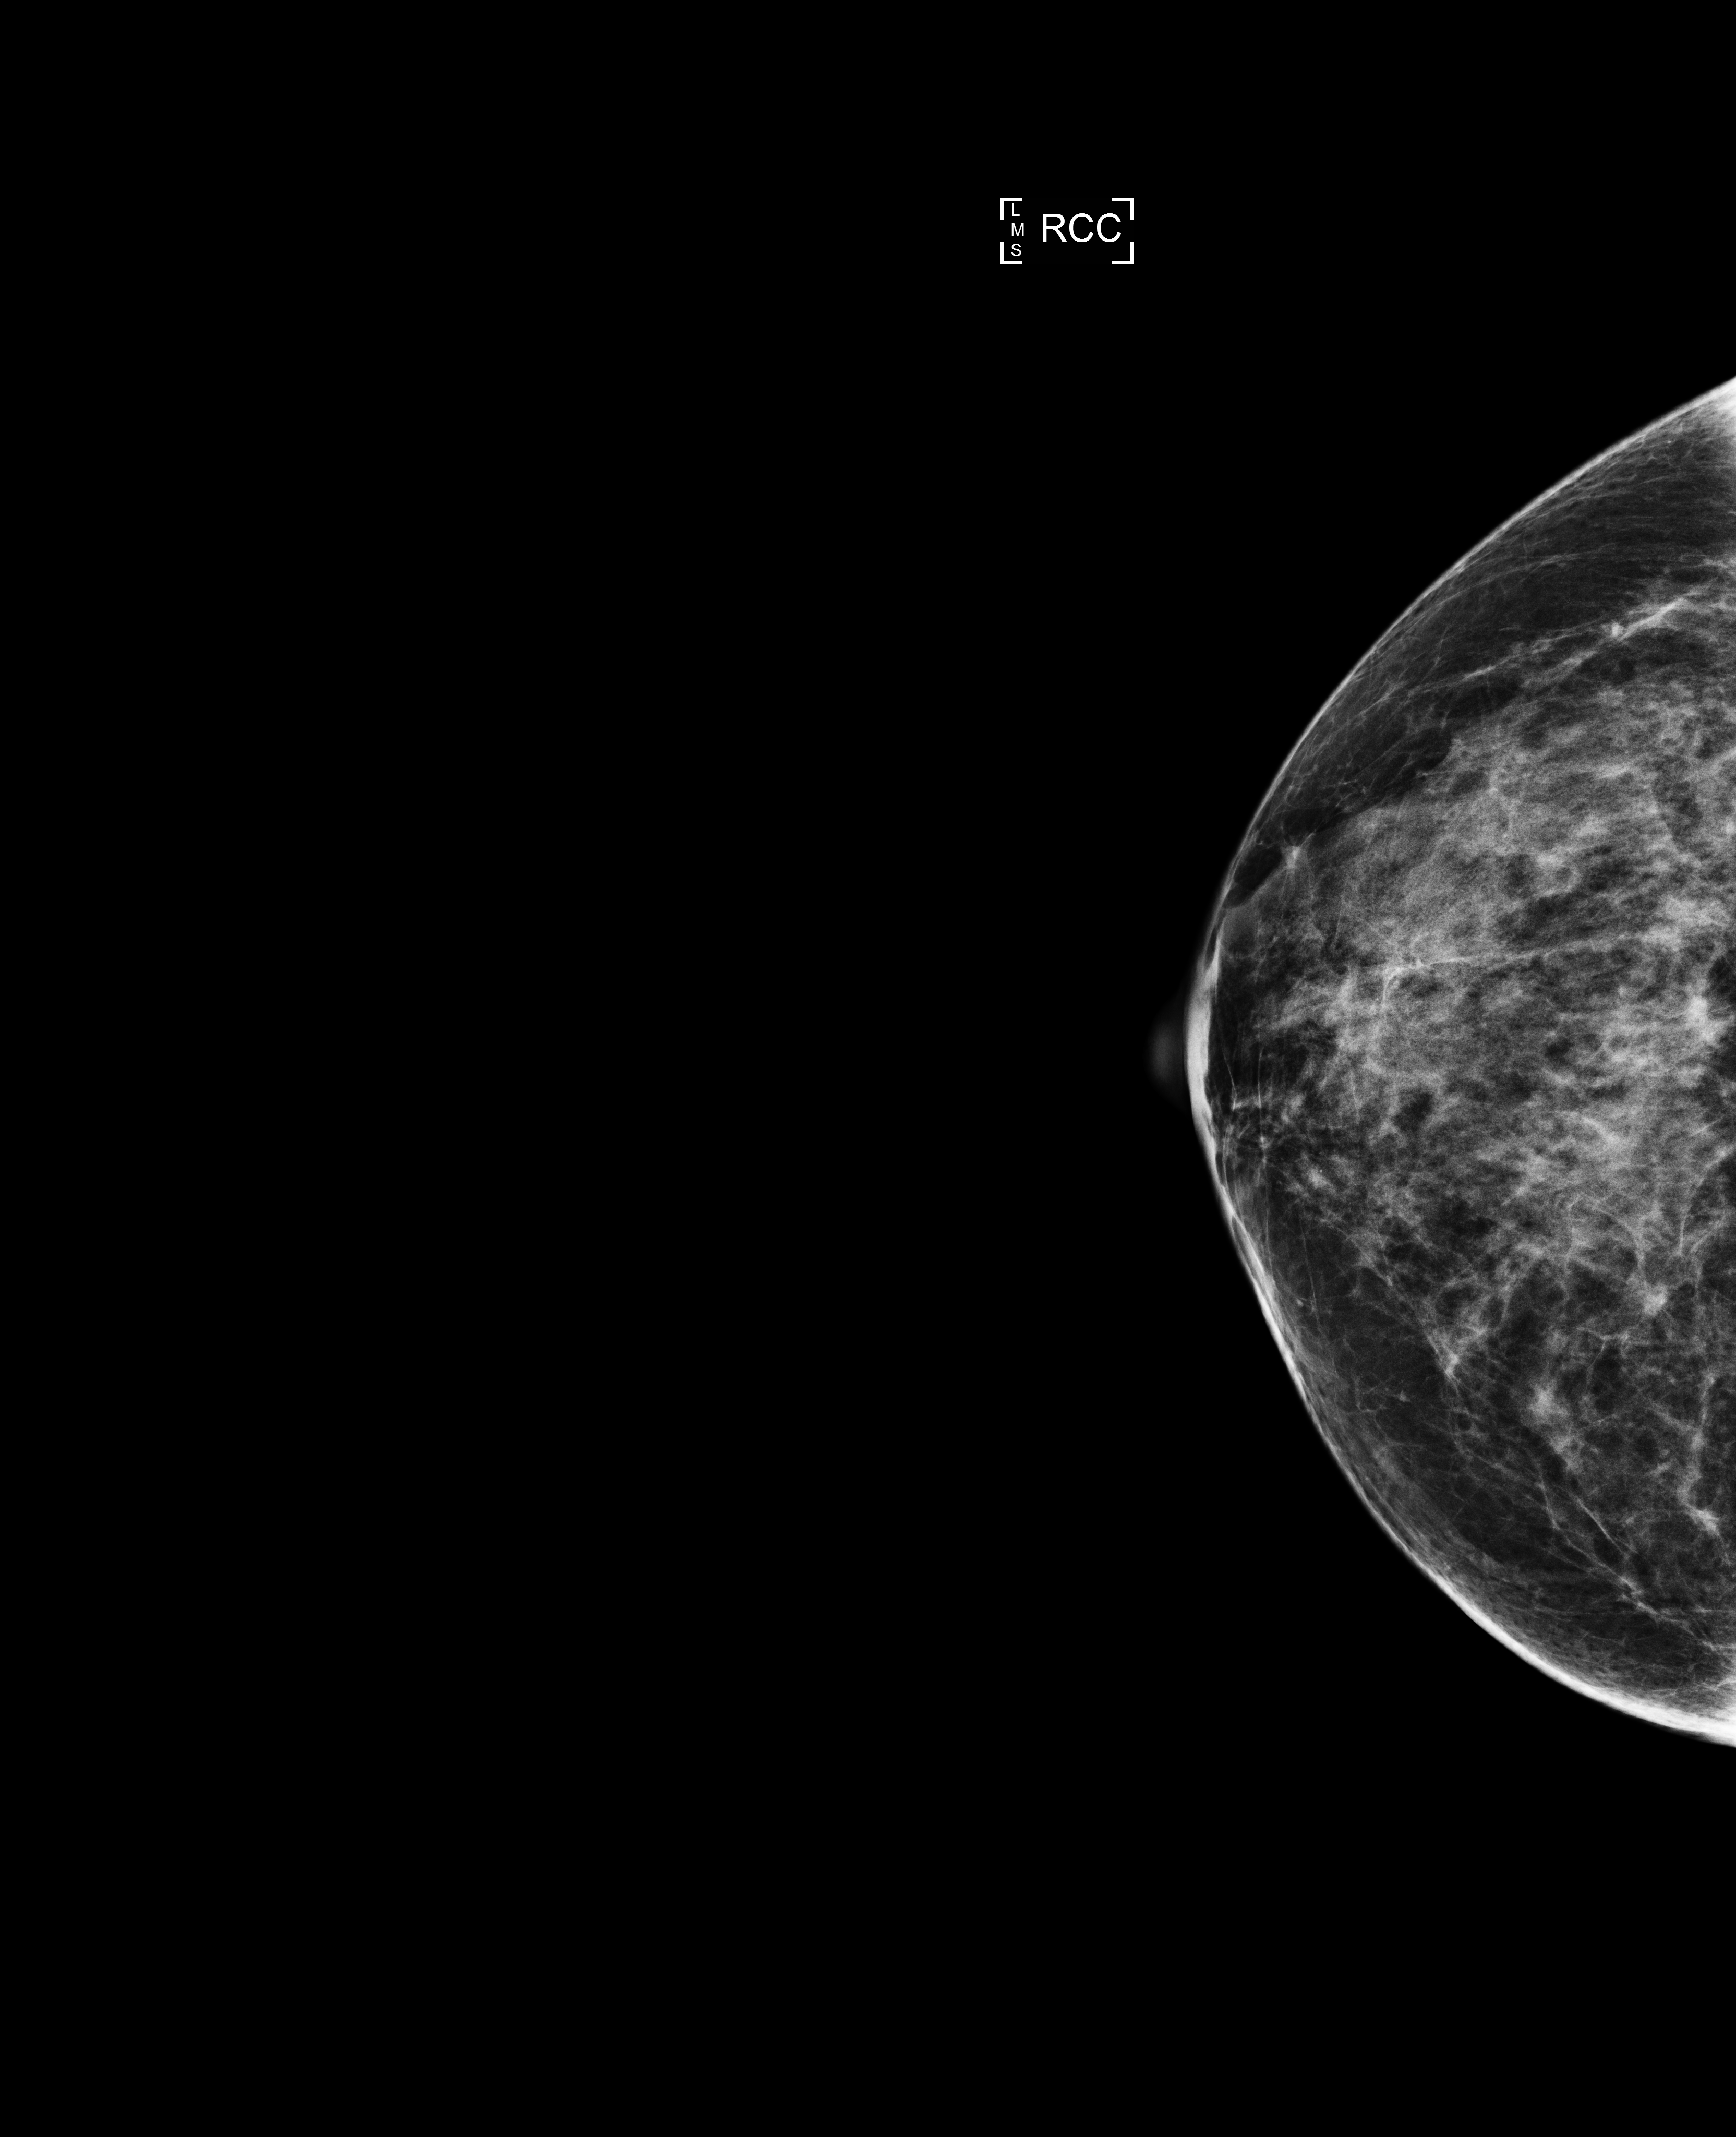
Annual screening mammography examination. Female patient, age 59 years.
Image type: full-field digital mammogram. Breast: right. Projection: CC view. BI-RADS breast density category at the screening exam (both breasts, scale 1–4): 3. Final BI-RADS category for the screening round (tomosynthesis exam, both breasts): category 1. Recall: no recall after this screen.